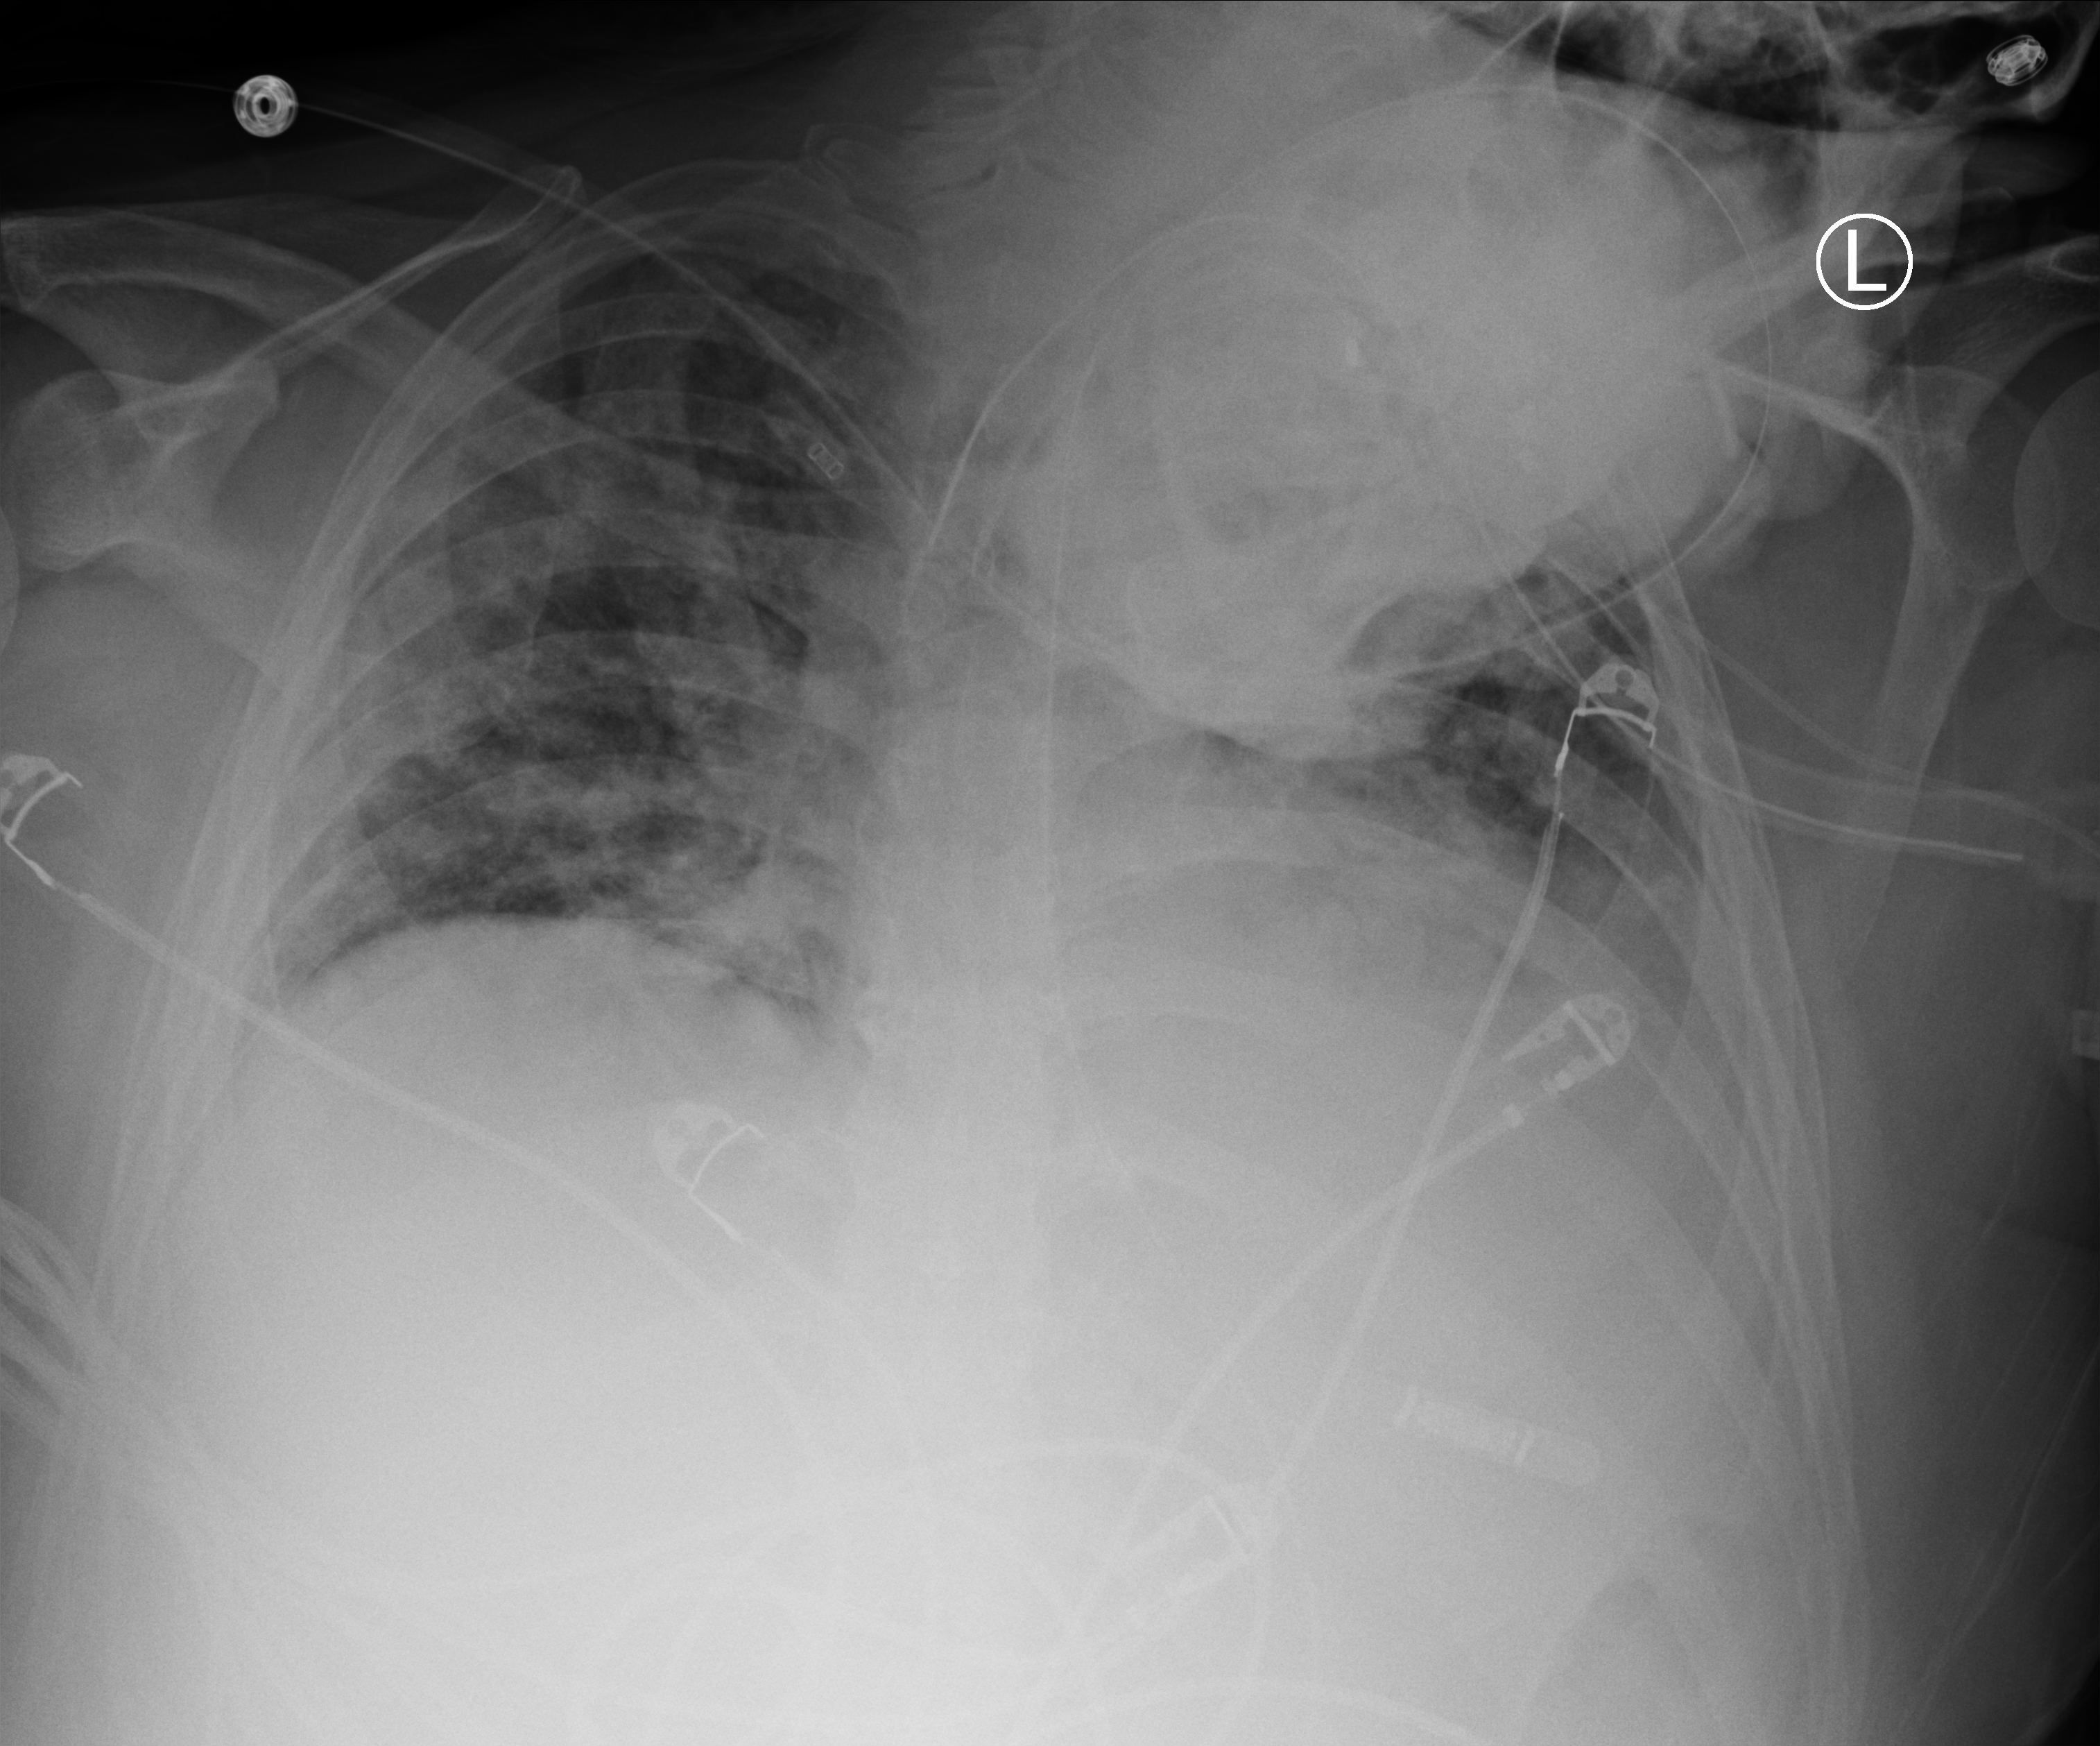
Portable chest radiograph; anteroposterior (AP) projection. Male patient hospitalised with COVID-19, age 18–59 years.
From the hospital-stay record, not from the radiograph (when in the stay this image was taken is not recorded):
- mechanically ventilated during this hospital stay: yes
- admitted to intensive care during this hospital stay: yes